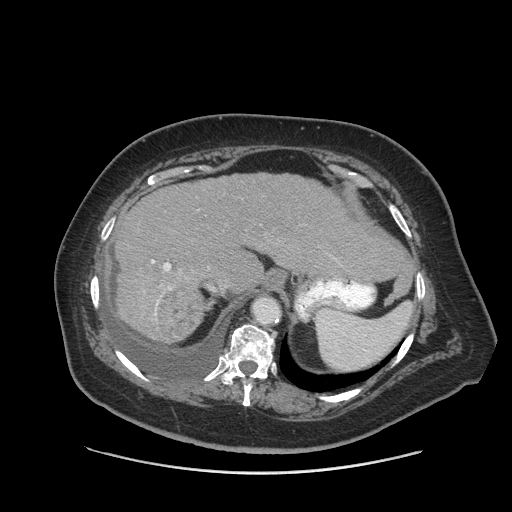
Contrast-enhanced abdominal CT (liver protocol), one axial slice. Position 63 of 91 along the scan axis. Reconstruction kernel STANDARD. 140 kVp. Soft-tissue window (W 400 / L 40 HU). 512 × 512 image matrix, field of view 420 × 420 mm. From the clinical record (not read from this slice): diagnosis: hepatocellular carcinoma (patient treated with transarterial chemoembolisation; whether this scan precedes or follows treatment is not stated here); TNM stage (as recorded): Stage-I; Child-Pugh class: A.
Outlined on this slice (semi-automatic segmentation, software-assisted and operator-edited):
- liver parenchyma outside the tumour (the mass and vessels are separate outlines, so this box may not span the whole liver): bounding box <114,172,404,342> (left, top, right, bottom; pixels)
- mass: <156,286,204,341>
- liver vessels: <151,259,171,271>